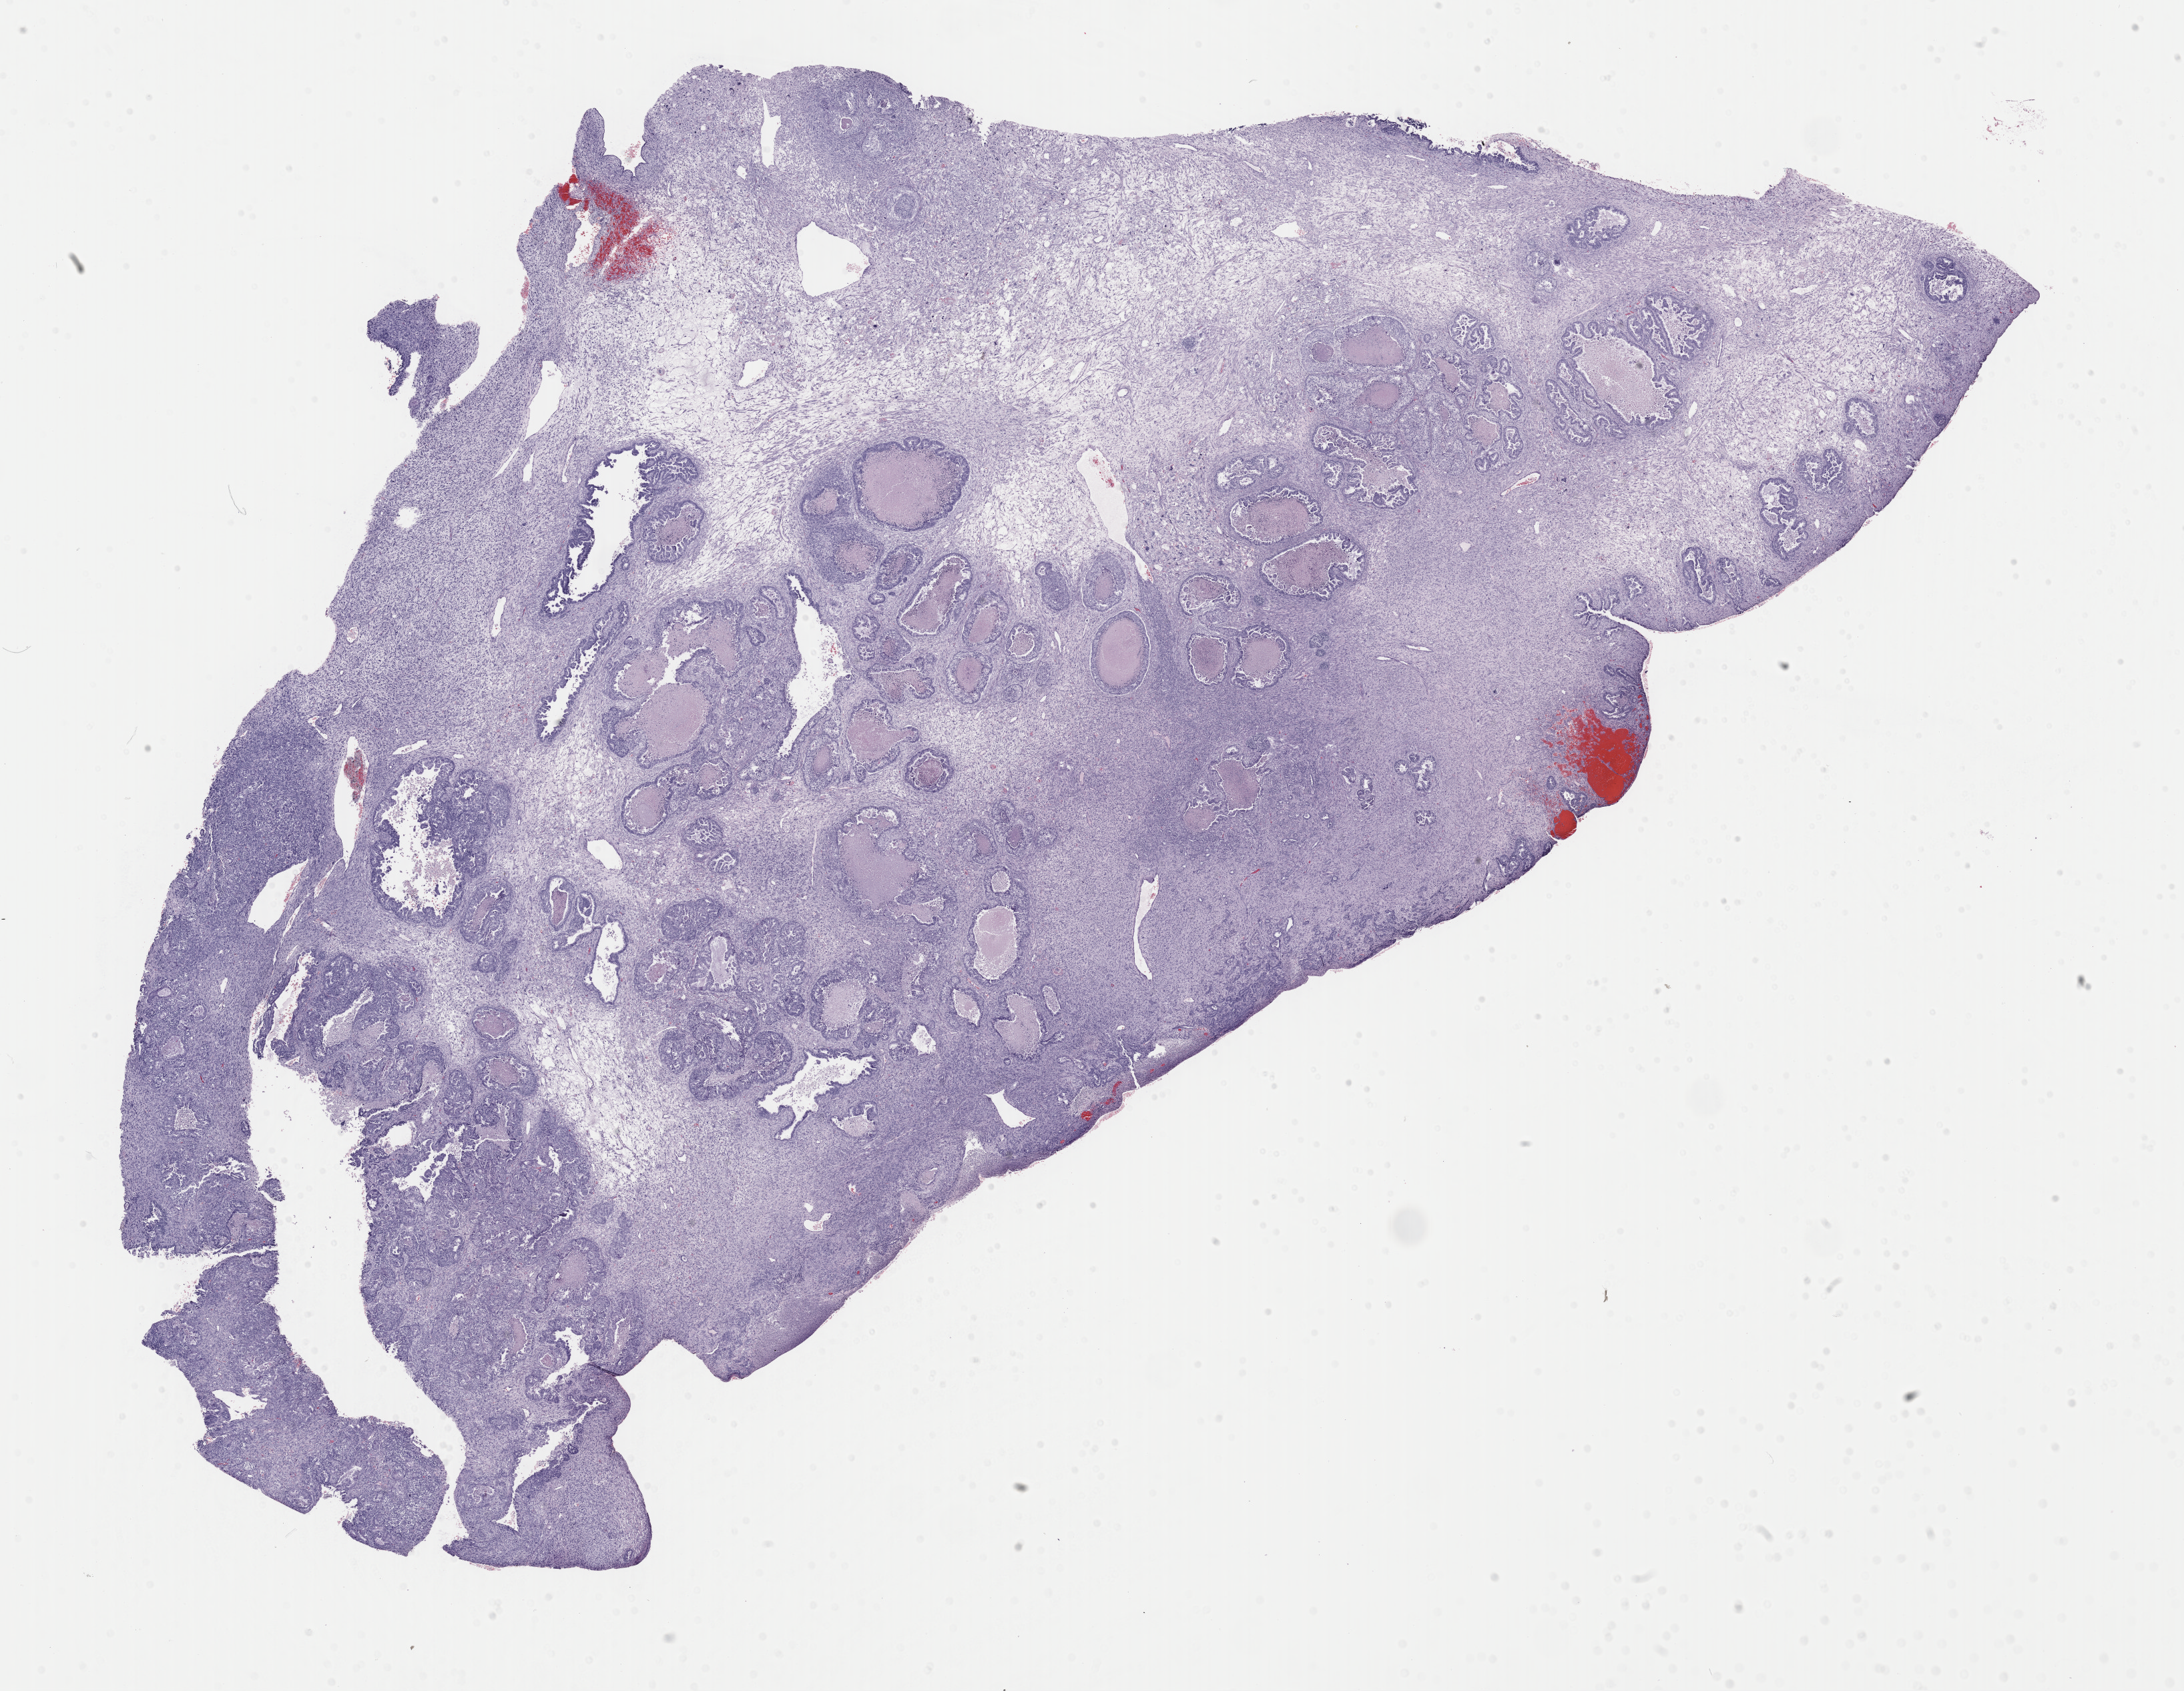
H&E whole-slide image — low-resolution overview of the scanned area, about 25.8 x 20.0 mm. FFPE section. Uterus, primary tumour sample. Female patient; age at initial diagnosis 68 years.
Pathologic diagnosis: Mullerian mixed tumor.